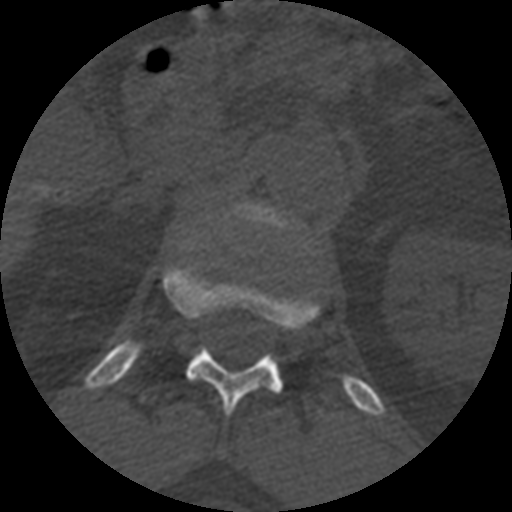
CT including the spine, one axial slice; reconstruction kernel STANDARD; bone window (W 1800 / L 400 HU); 1.25 mm slice thickness; 512 × 512 image matrix, field of view 160 × 160 mm. Patient age 71 years. From the clinical record (not read from this slice): primary cancer: prostate.
Outlined on this slice (semi-automatic segmentation, software-assisted and operator-edited):
- L1 vertebra: bounding box [x1, y1, x2, y2] px = [225, 201, 295, 233]
- T12 vertebra: [164, 265, 320, 417]